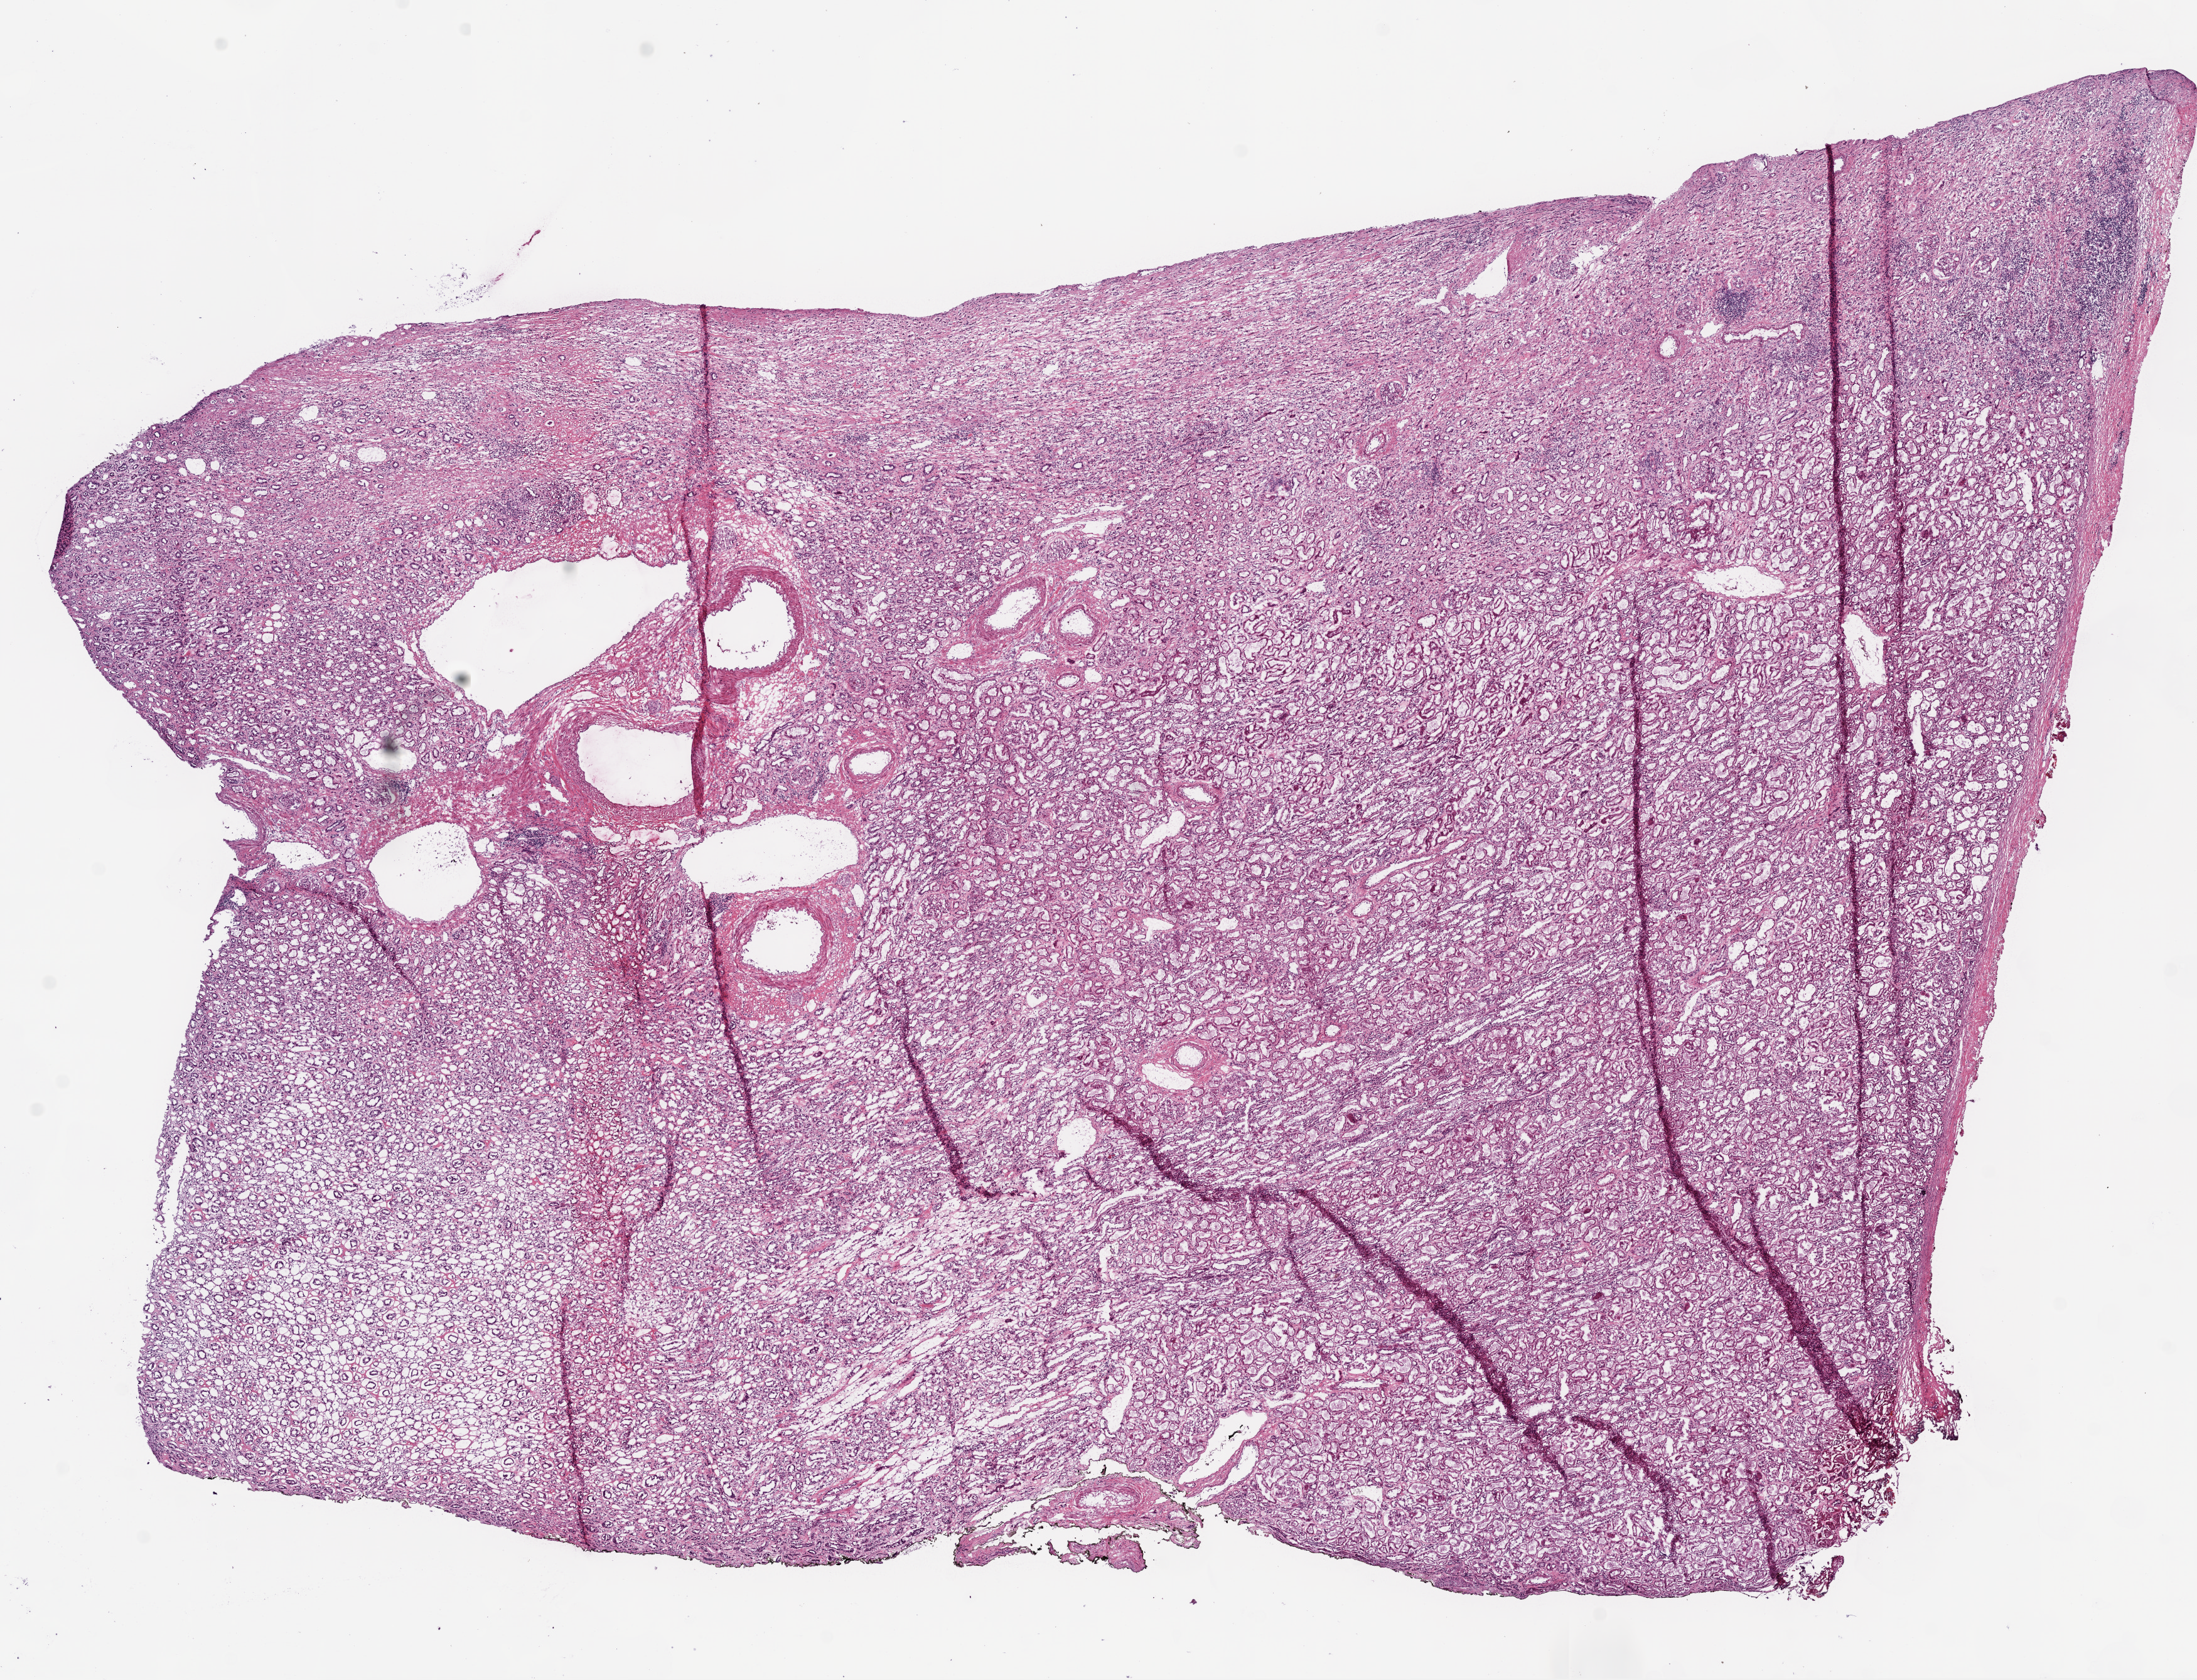
Digitized H&E tissue section (whole slide) — low-resolution overview of the scanned area, about 14.0 x 10.7 mm; frozen section; solid tissue normal (non-tumour tissue) sample from the kidney. Patient: male, age at initial diagnosis 36 years.
This section: solid tissue normal sample (biorepository sample class). Patient diagnosis: Clear cell adenocarcinoma, NOS.